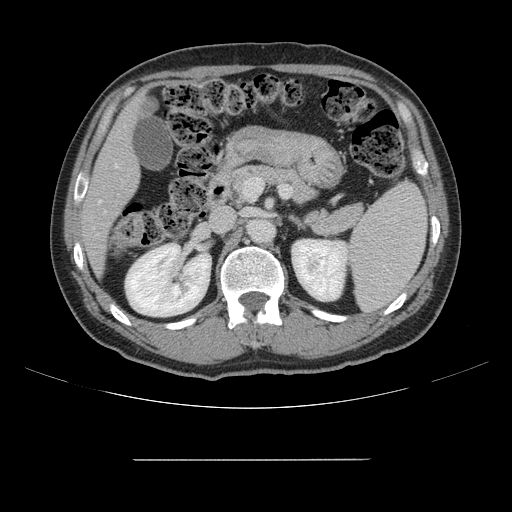
Contrast-enhanced abdominal CT, one axial slice; position 74 of 164 along the scan axis; intravenous contrast given; soft-tissue window (W 400 / L 40 HU); 2.5 mm slice thickness; 512 × 512 image matrix. Male patient, age 54 years. From the clinical record (not read from this slice): diagnosis: colorectal cancer liver metastases, imaged before liver resection; multiple liver metastases: yes; largest metastasis: 1 cm; disease in both lobes: no.
Structures marked on this image (manually delineated by an expert):
- hepatic veins: bounding box <98,164,118,203> (left, top, right, bottom; pixels)
- liver: <85,101,141,272>
- planned liver remnant (the part of the liver to remain after resection): <85,101,140,273>